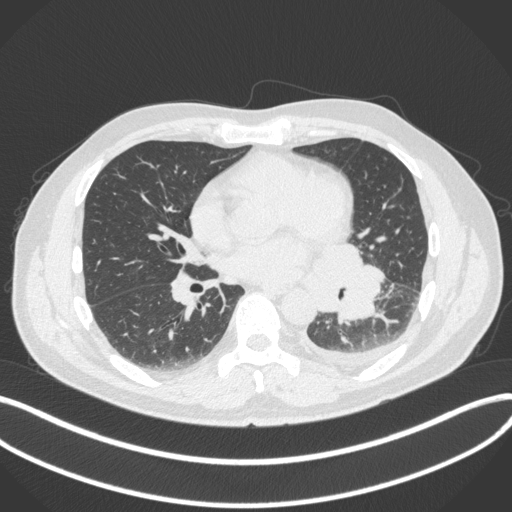
Chest CT, one axial slice; slice 168 of 350 in the series (ordered by position); 120 kVp; lung window (W 1500 / L -600 HU); 1 mm slice thickness; 512 × 512 image matrix. Patient: male, 58 years. Case-level facts recorded for this patient, not image findings: clinical TNM (as recorded): T3 N1 M1b; histopathological grade: G3.
Annotated regions visible in this slice (rectangle marked by the reading radiologist):
- lung tumour (recorded histology: small cell carcinoma): bounding box [x1, y1, x2, y2] px = [315, 243, 385, 326]